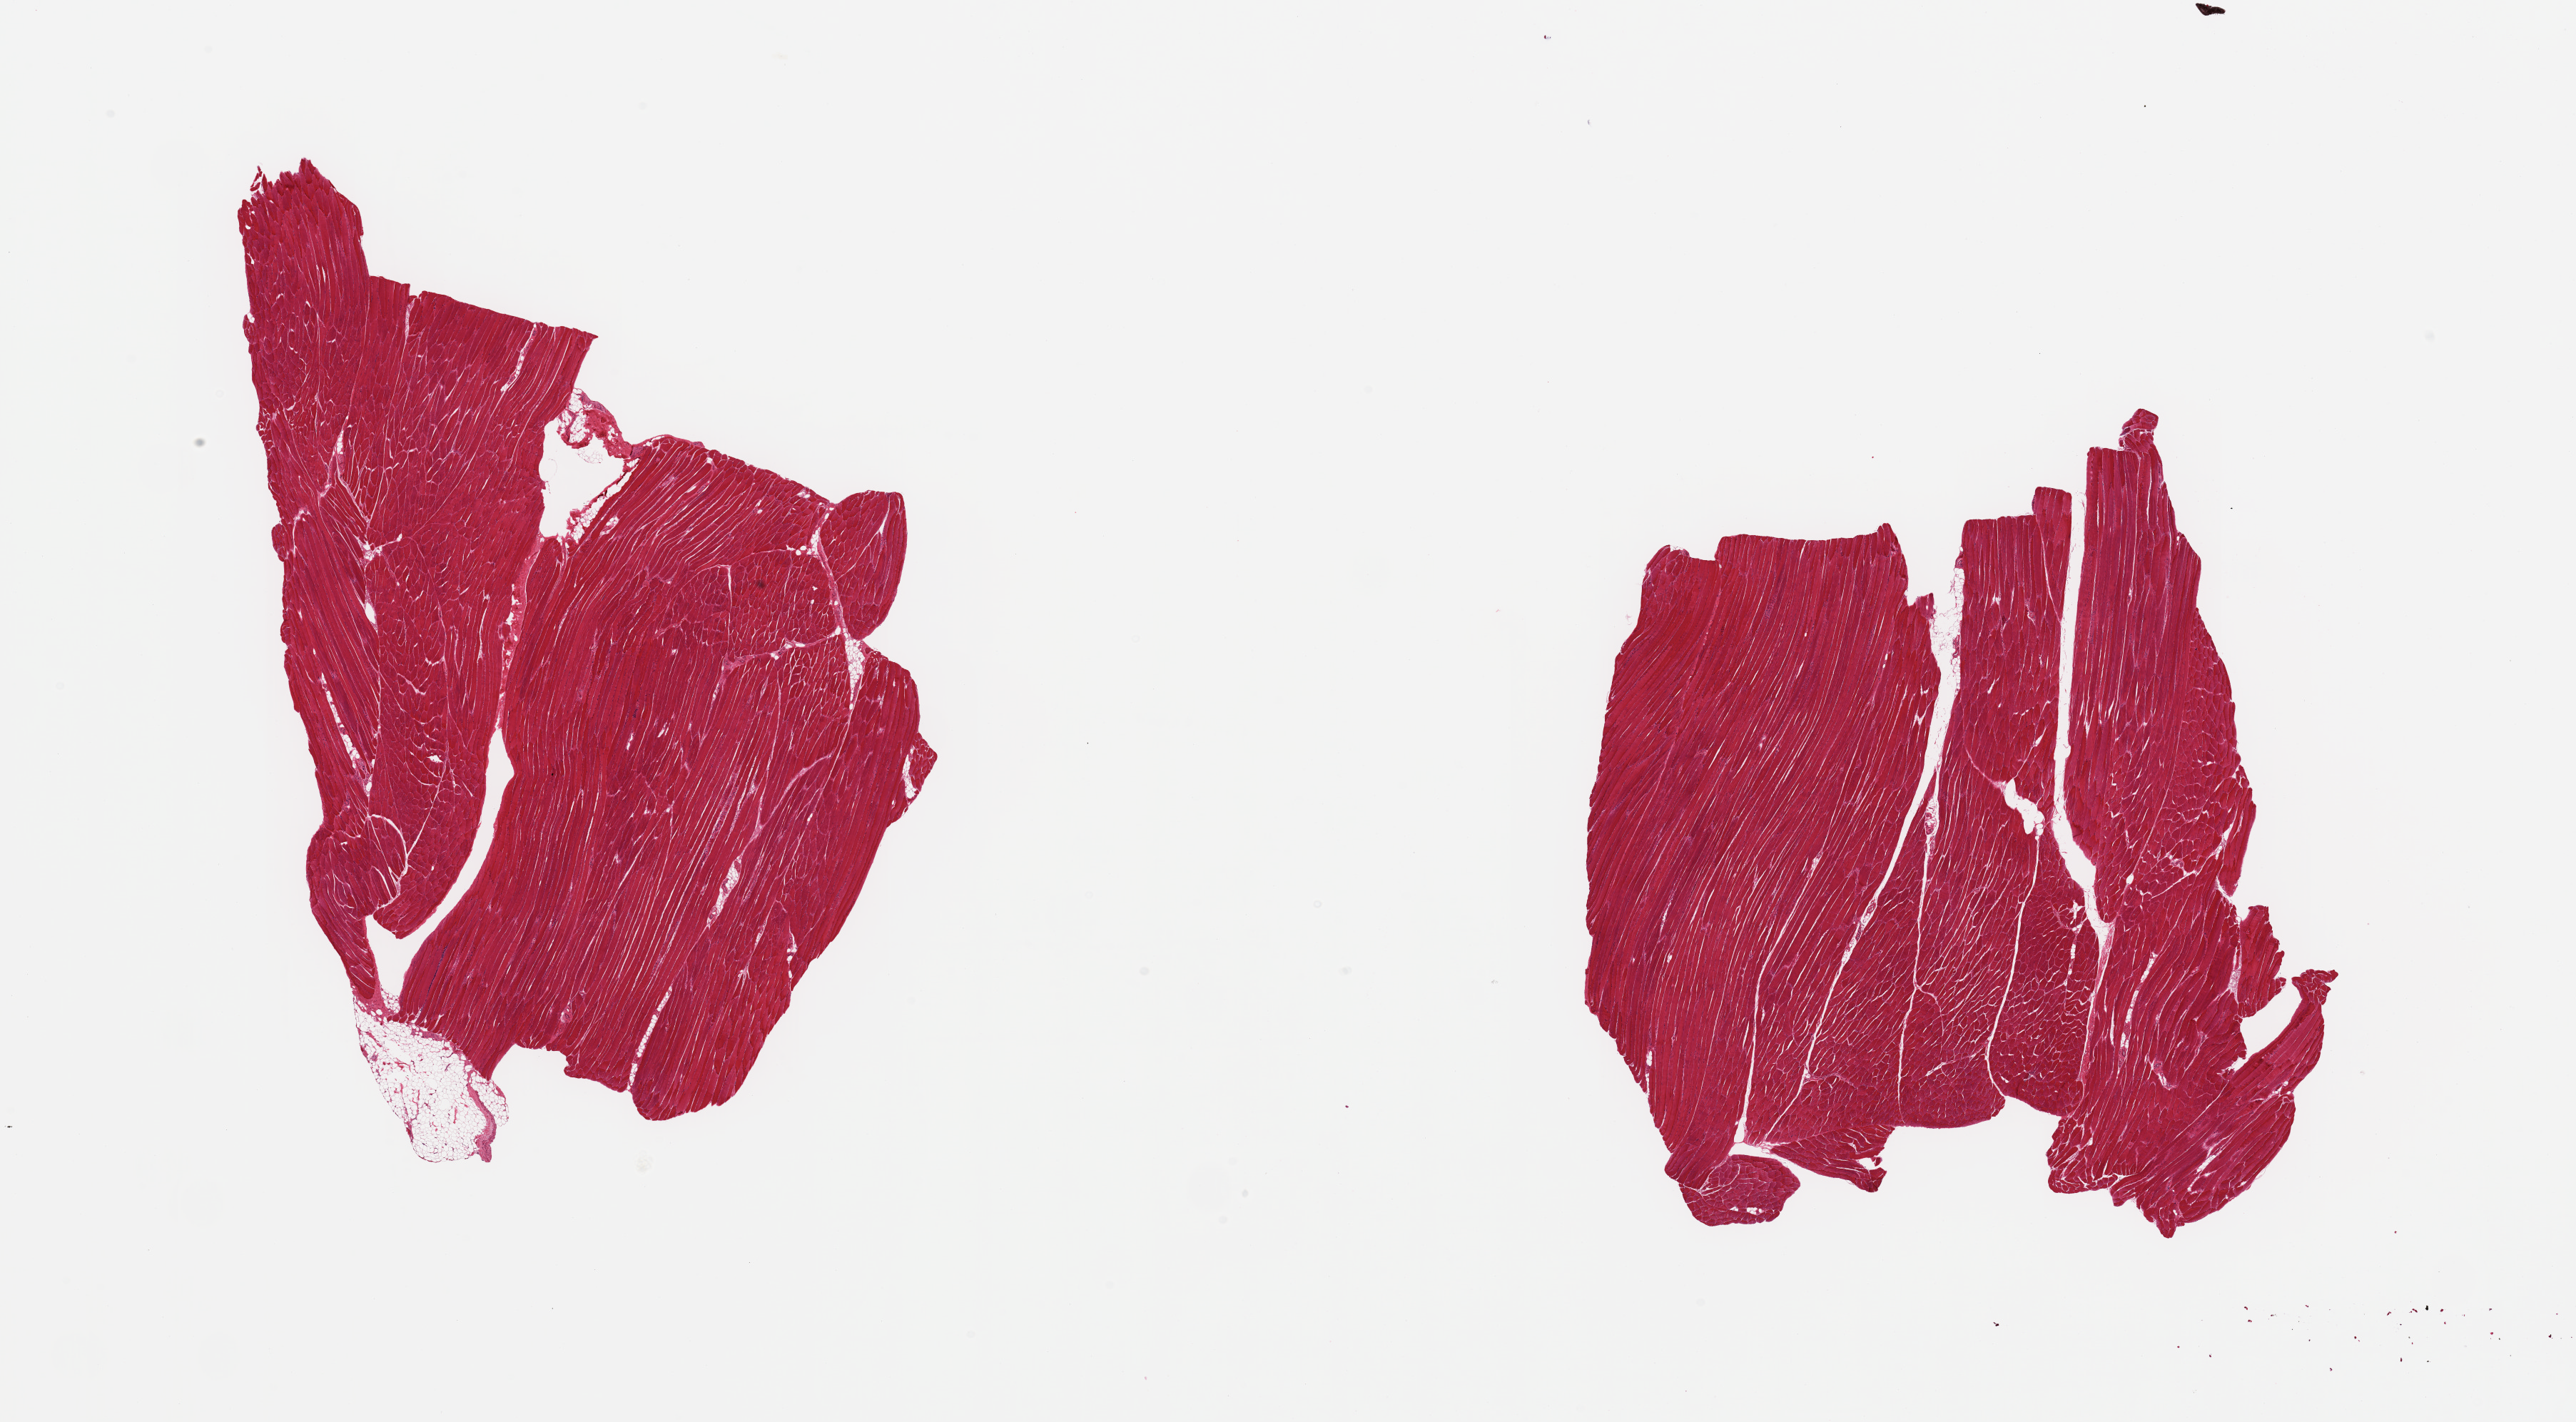
Hematoxylin and eosin (H&E) whole-slide image — shown as a low-resolution overview of the whole scanned area (about 28.5 x 15.8 mm, from a 20x scan), PAXgene-fixed, paraffin-embedded tissue, sampled site (target tissue): skeletal muscle, donor tissue sample. Male donor.
Reviewer comment on this tissue sample: 2 pieces; 1.7 mm fat at edge of 1 piece.